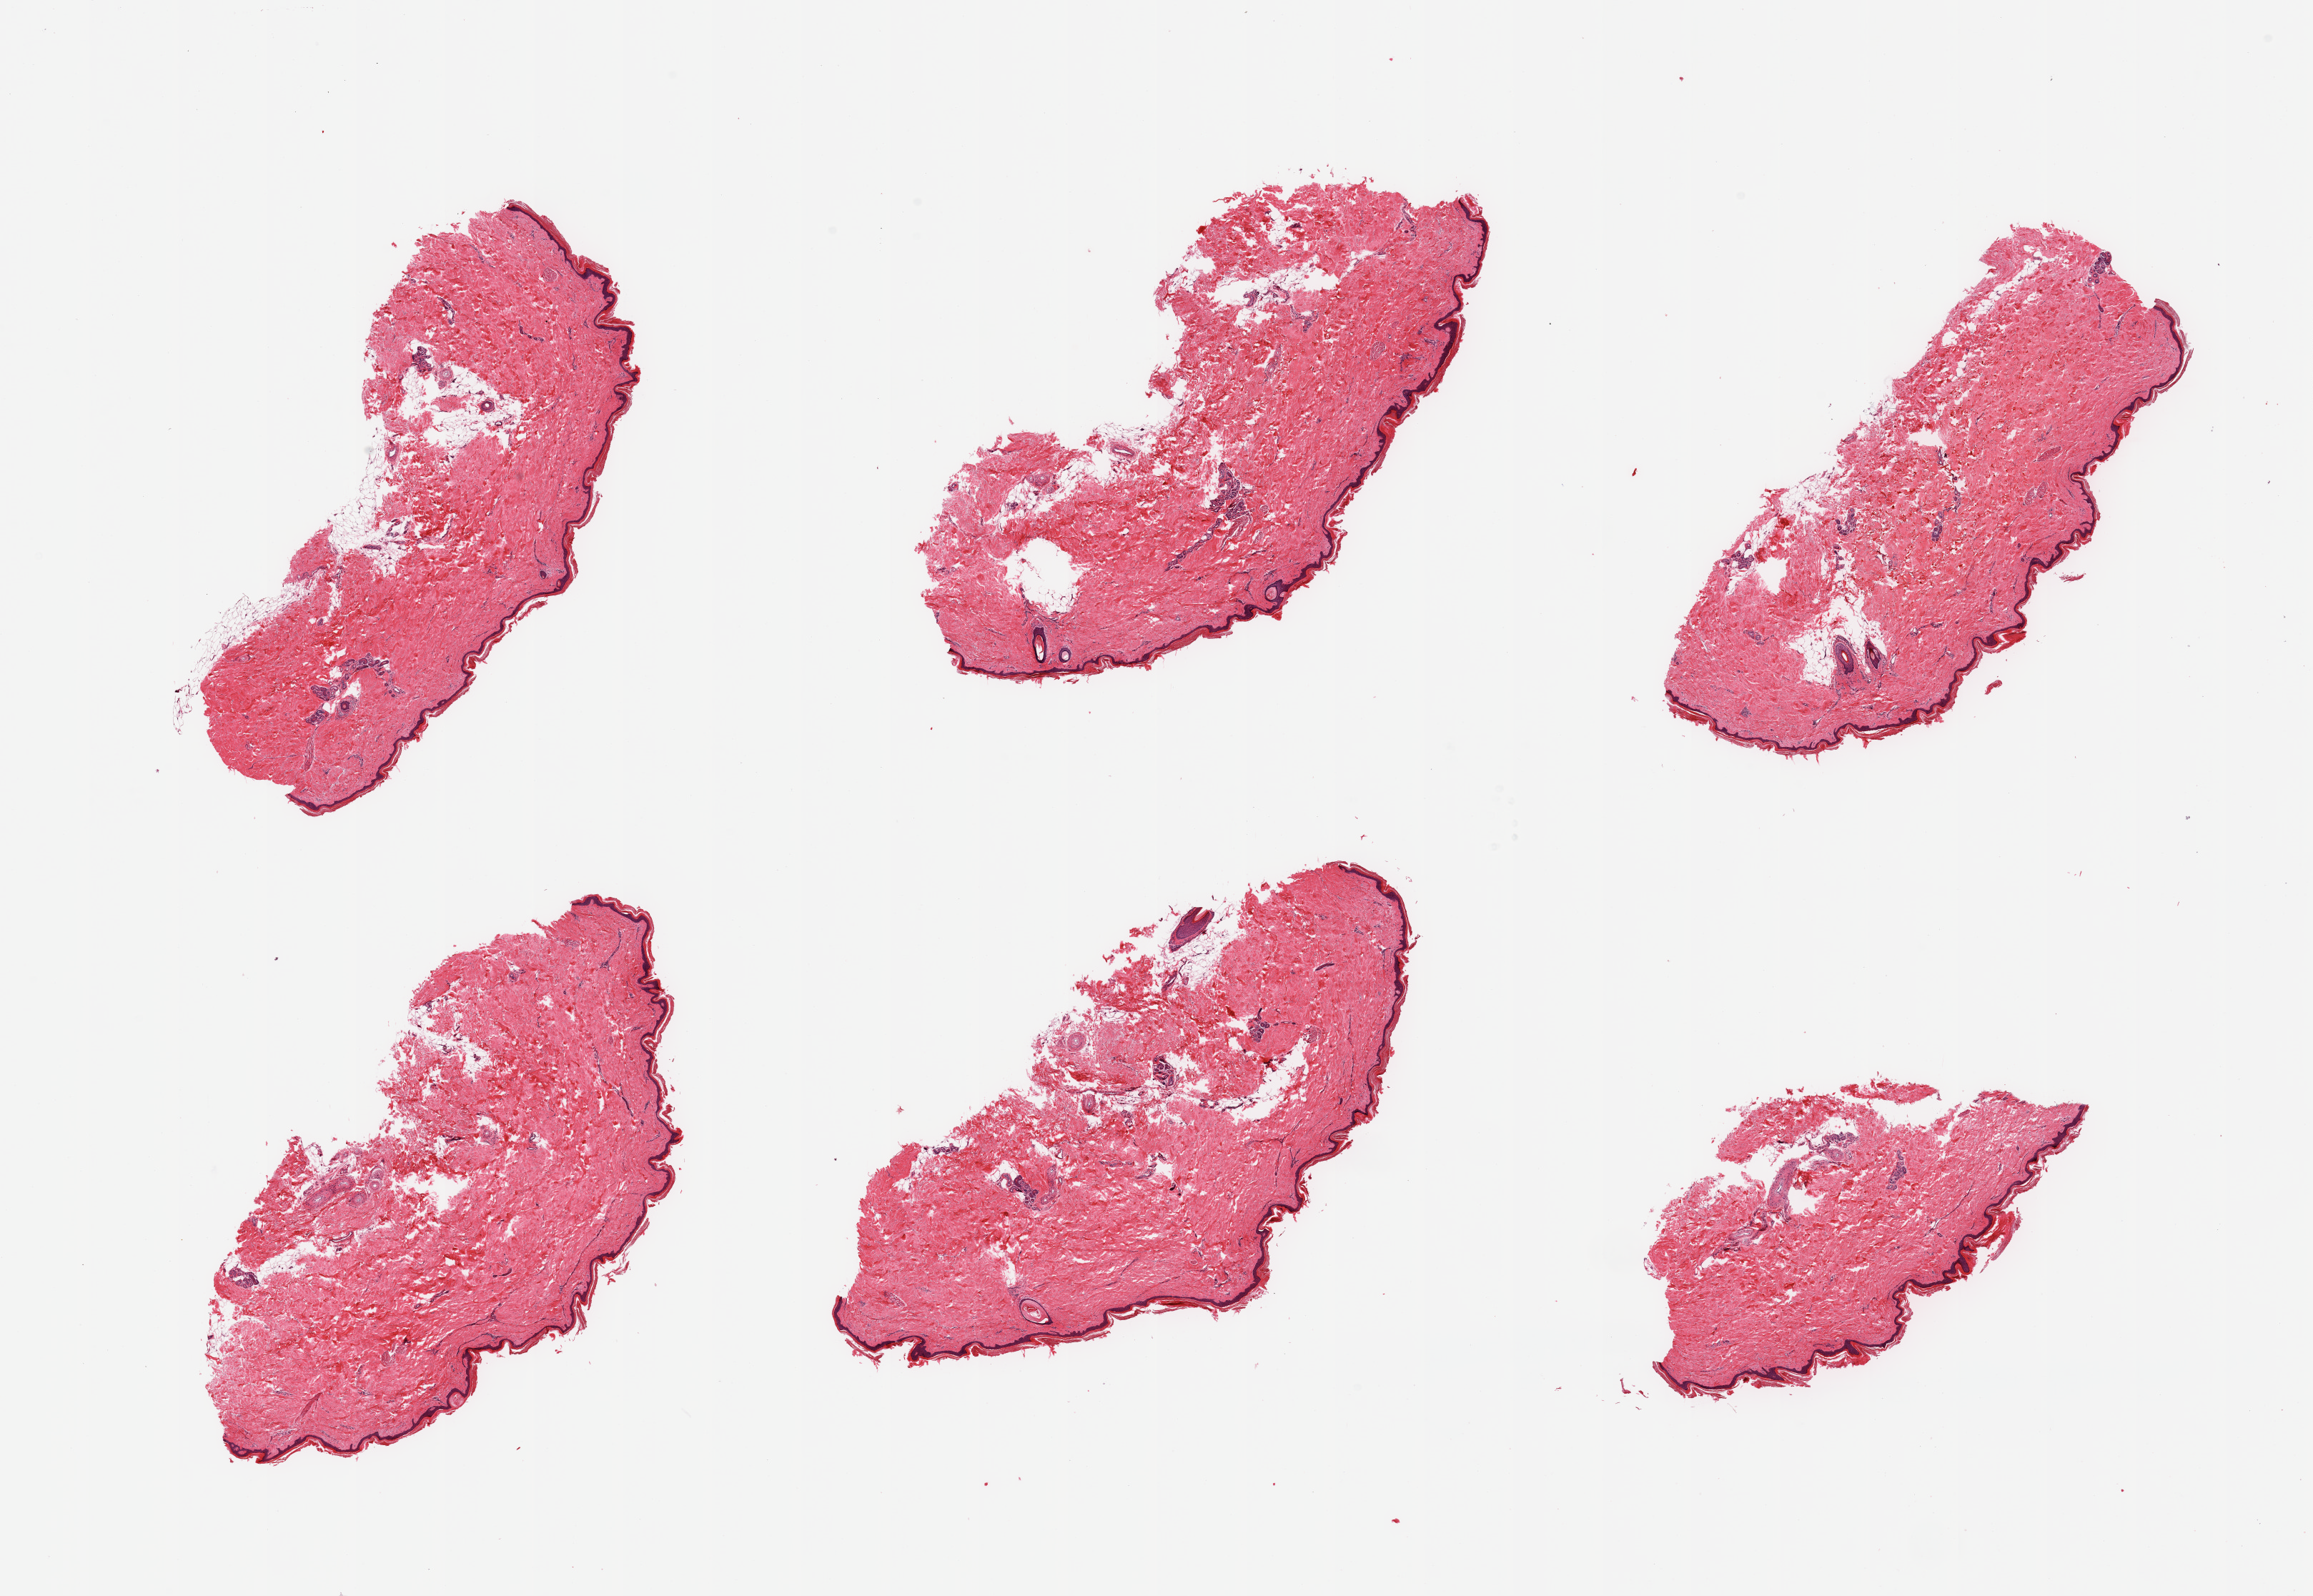
Digitized H&E-stained section — low-resolution overview of the scanned area, about 25.6 x 17.7 mm (acquisition: 20x scan), PAXgene-fixed paraffin-embedded (PFPE) section, target tissue: skin of lower leg, tissue donor sample. Donor: female.
• reviewer comment on this tissue sample: 6 pieces, no significant dermal fat; squamous epithelium is 30-40 microns